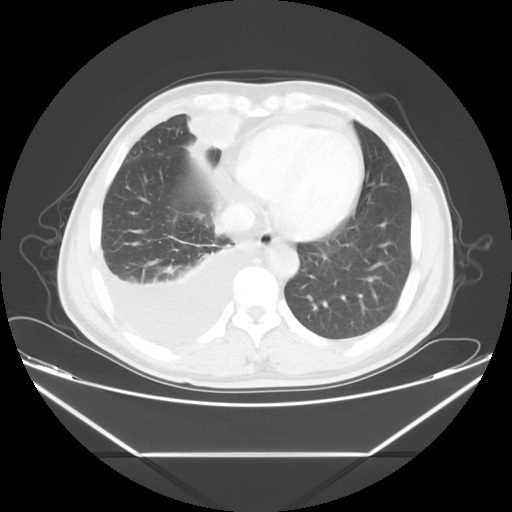
Chest CT, one axial slice. Slice 16 of 56 in the series (ordered by position). 120 kVp. Lung window (W 1500 / L -600 HU). 512 × 512 image matrix, field of view 412 × 412 mm. Male patient, age 57 years. Case-level facts recorded for this patient, not image findings: clinical TNM (as recorded): T2 N3 M1.
Annotated regions visible in this slice (rectangle marked by the reading radiologist):
- lung tumour (recorded histology: adenocarcinoma): bounding box [x1, y1, x2, y2] px = [186, 107, 242, 148]